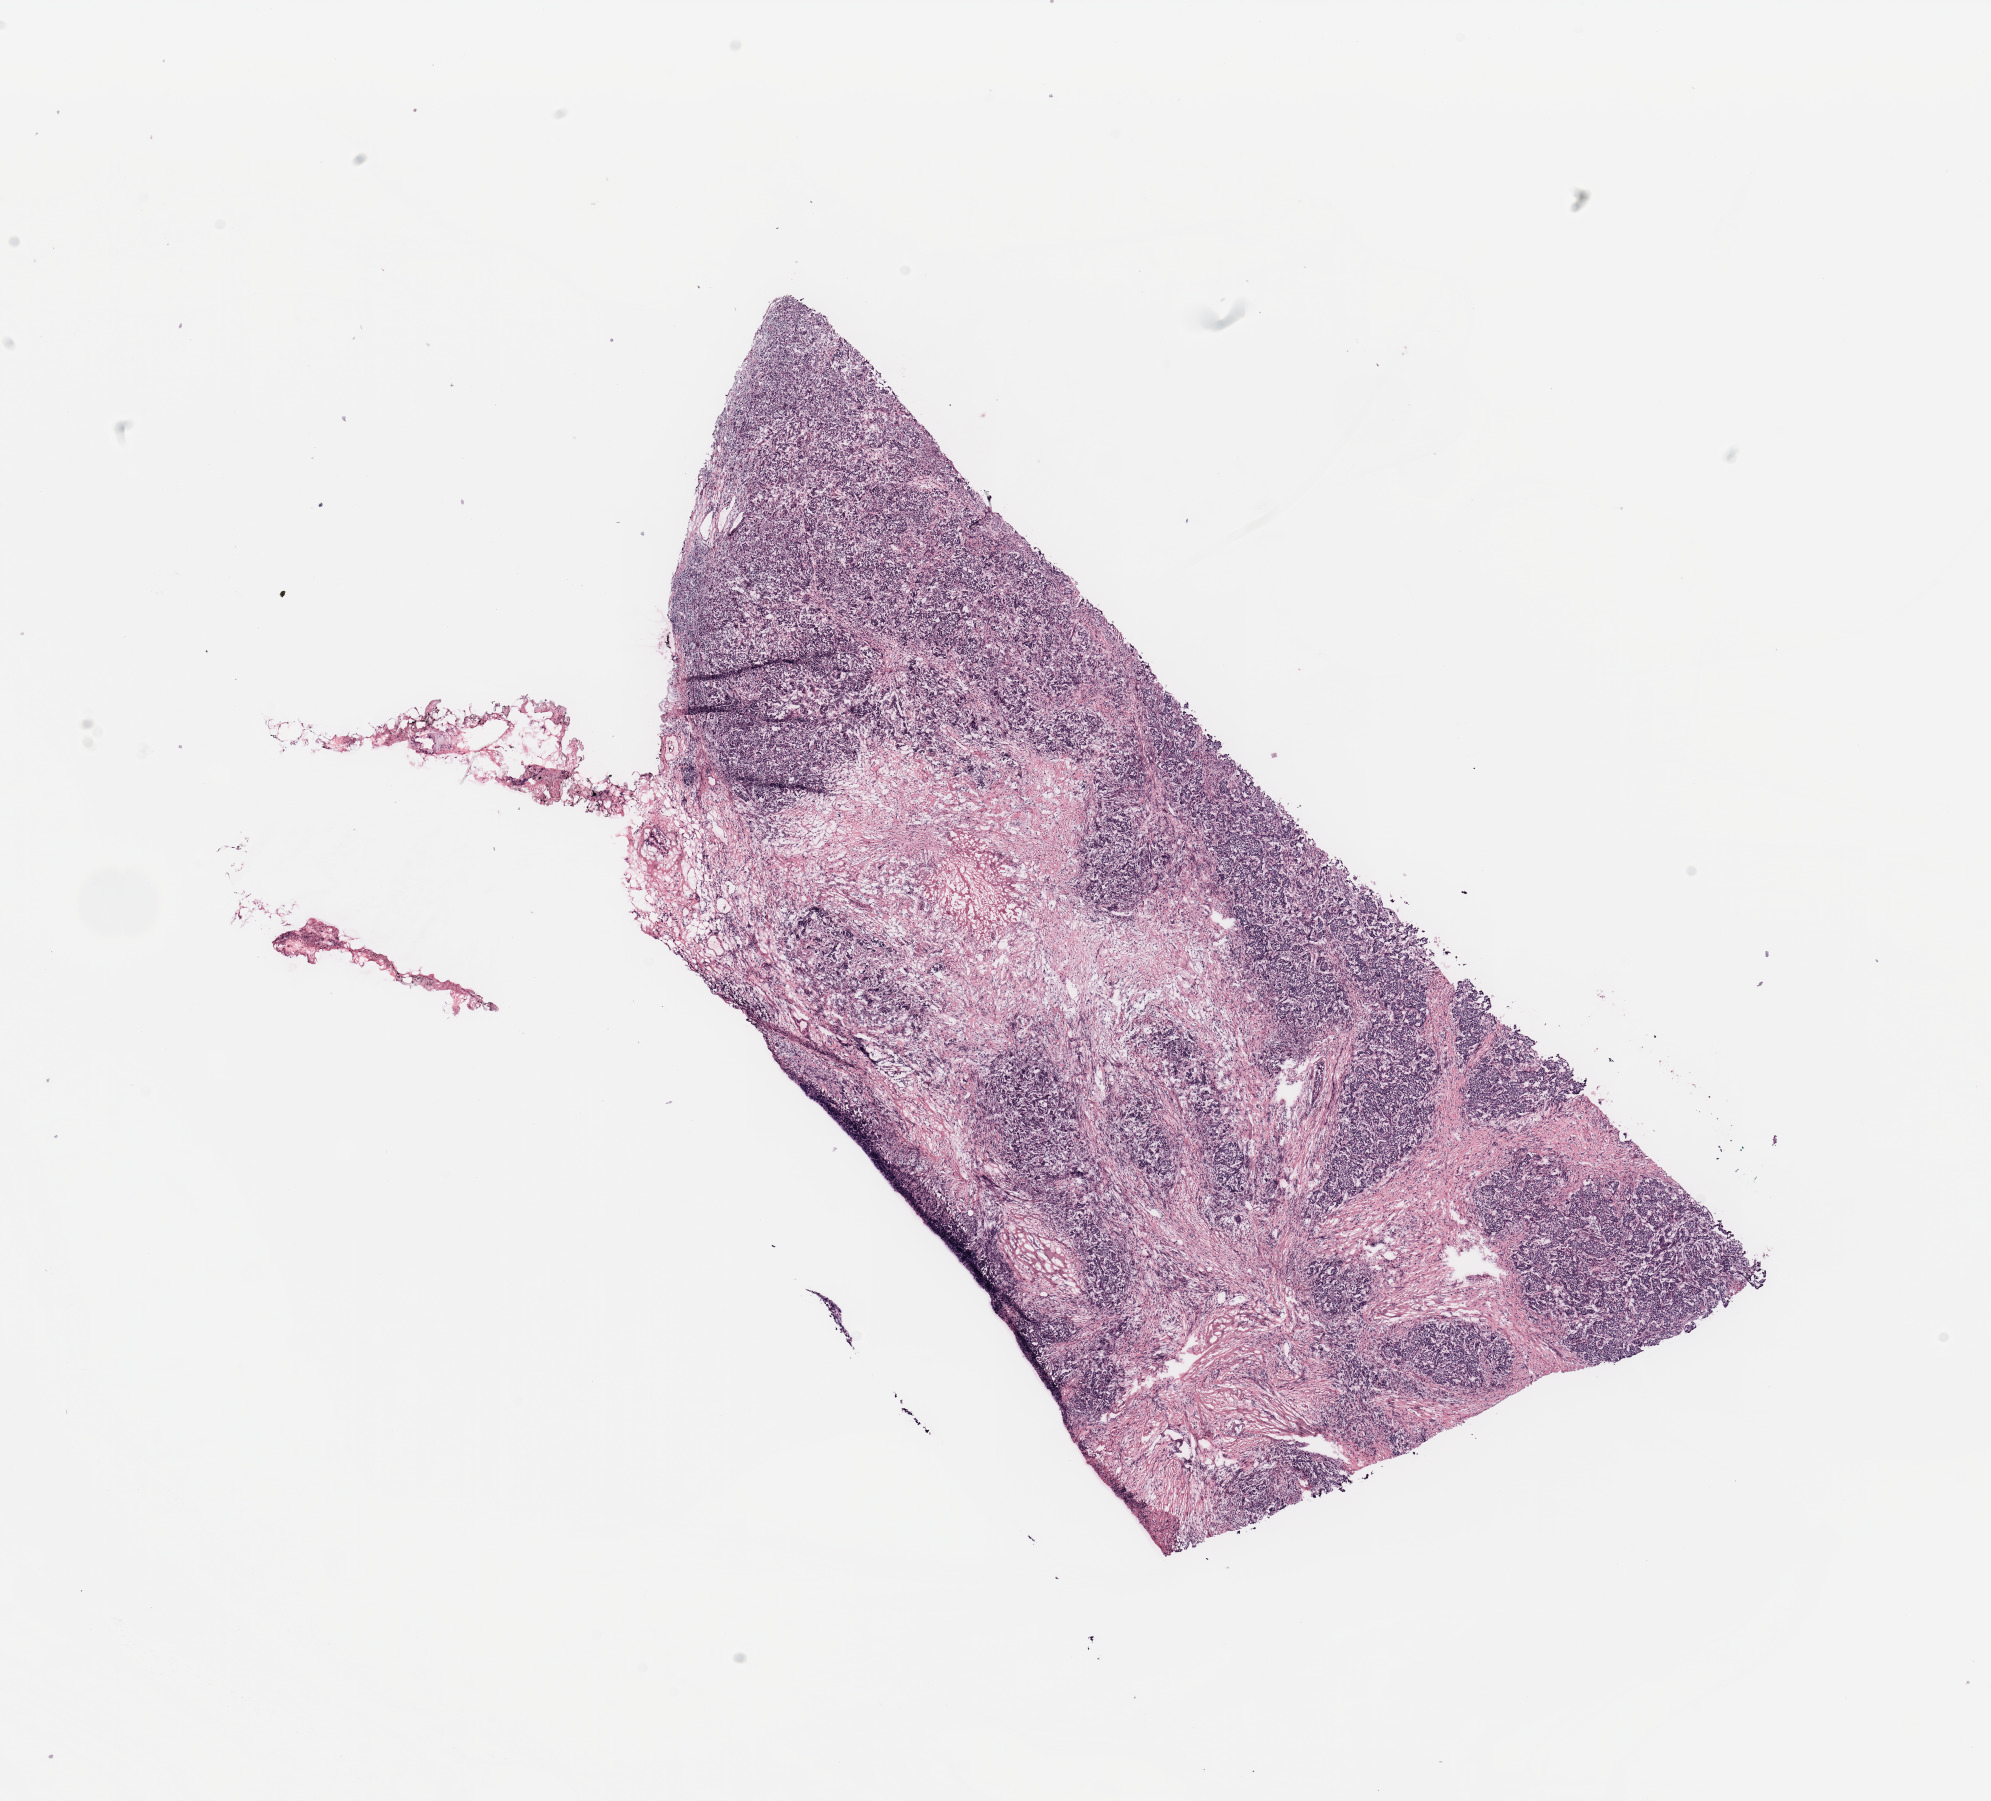
Whole-slide histology image, Hematoxylin and eosin (H&E) stained, whole scanned area (about 15.8 x 14.2 mm, acquisition: 20x scan) shown as a low-resolution overview. 86-year-old female patient.
Specimen: tumour tissue sample, breast.